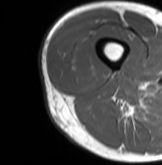
MRI of an extremity soft-tissue mass, one axial slice; position 14 of 61 along the scan axis; MR volume resampled by the dataset authors to the PET/CT grid (not the native acquisition matrix); 162 × 165 image matrix, field of view 158 × 161 mm. Male patient. From the clinical record (not read from this slice): histological type: poorly differentiated synovial sarcoma; grade: high; site of the primary tumour: right buttock.
Structures marked on this image (expert contour drawn on MRI and transferred to this co-registered scan by the dataset authors):
- gross tumour volume including surrounding oedema: bounding box <62,47,94,82> (left, top, right, bottom; pixels)